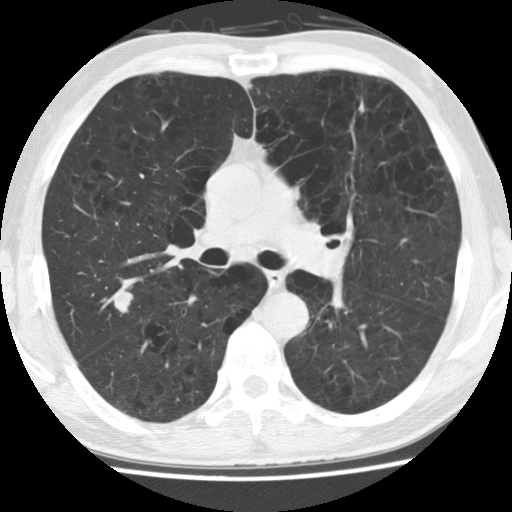
Low-dose screening chest CT, one axial slice; position 91 of 158 along the scan axis; 120 kVp; lung window (W 1500 / L -600 HU); 512 × 512 image matrix, field of view 324 × 324 mm.
Outlined on this slice (expert manual segmentation):
- lesion 1 (tumor, upper lobe of right lung): bounding box <113,291,133,313> (left, top, right, bottom; pixels)